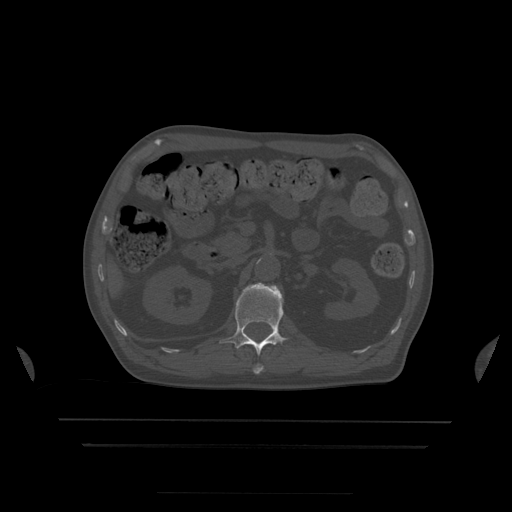
CT including the spine, one axial slice; slice 170 of 522 in the series (ordered by position); bone window (W 1800 / L 400 HU); 1.25 mm slice thickness; 512 × 512 image matrix. Patient age 68 years. Case-level facts recorded for this patient, not image findings: primary cancer: urothelial.
Outlined on this slice (semi-automatic segmentation, software-assisted and operator-edited):
- L1 vertebra: bounding box [x1, y1, x2, y2] px = [220, 283, 288, 374]